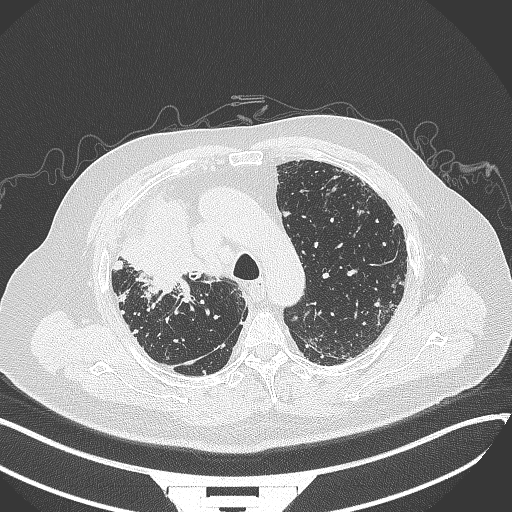
Chest CT, one axial slice; position 261 of 384 along the scan axis; reconstruction kernel B70f; lung window (W 1500 / L -600 HU); 512 × 512 image matrix, field of view 400 × 400 mm. Patient: male, 69 years. Case-level facts recorded for this patient, not image findings: clinical TNM (as recorded): T4 N3 M1.
Annotated regions visible in this slice (rectangle marked by the reading radiologist):
- lung tumour (recorded histology: adenocarcinoma): bounding box [x1, y1, x2, y2] px = [115, 193, 216, 300]